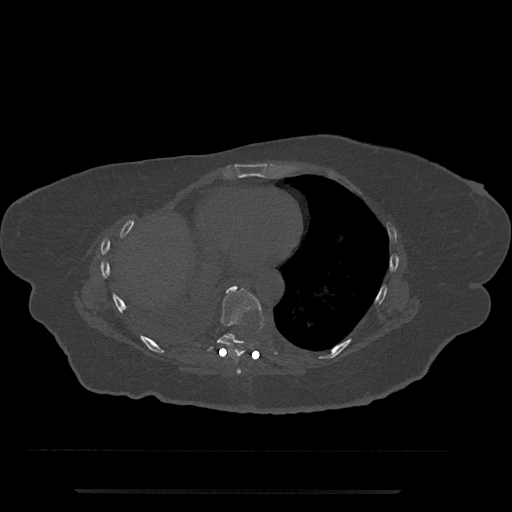
CT including the spine, one axial slice. Slice 384 of 797 in the series (ordered by position). 120 kVp. Bone window (W 1800 / L 400 HU). 512 × 512 image matrix, field of view 440 × 440 mm. Patient: female, 51 years. From the clinical record (not read from this slice): primary cancer: neuro; vertebrae with lytic lesions (as recorded): T8.
Outlined on this slice (semi-automatically segmented with operator editing):
- T7 vertebra: bounding box <237,368,241,375> (left, top, right, bottom; pixels)
- T8 vertebra: <207,286,264,357>
- T9 vertebra: <227,333,235,340>